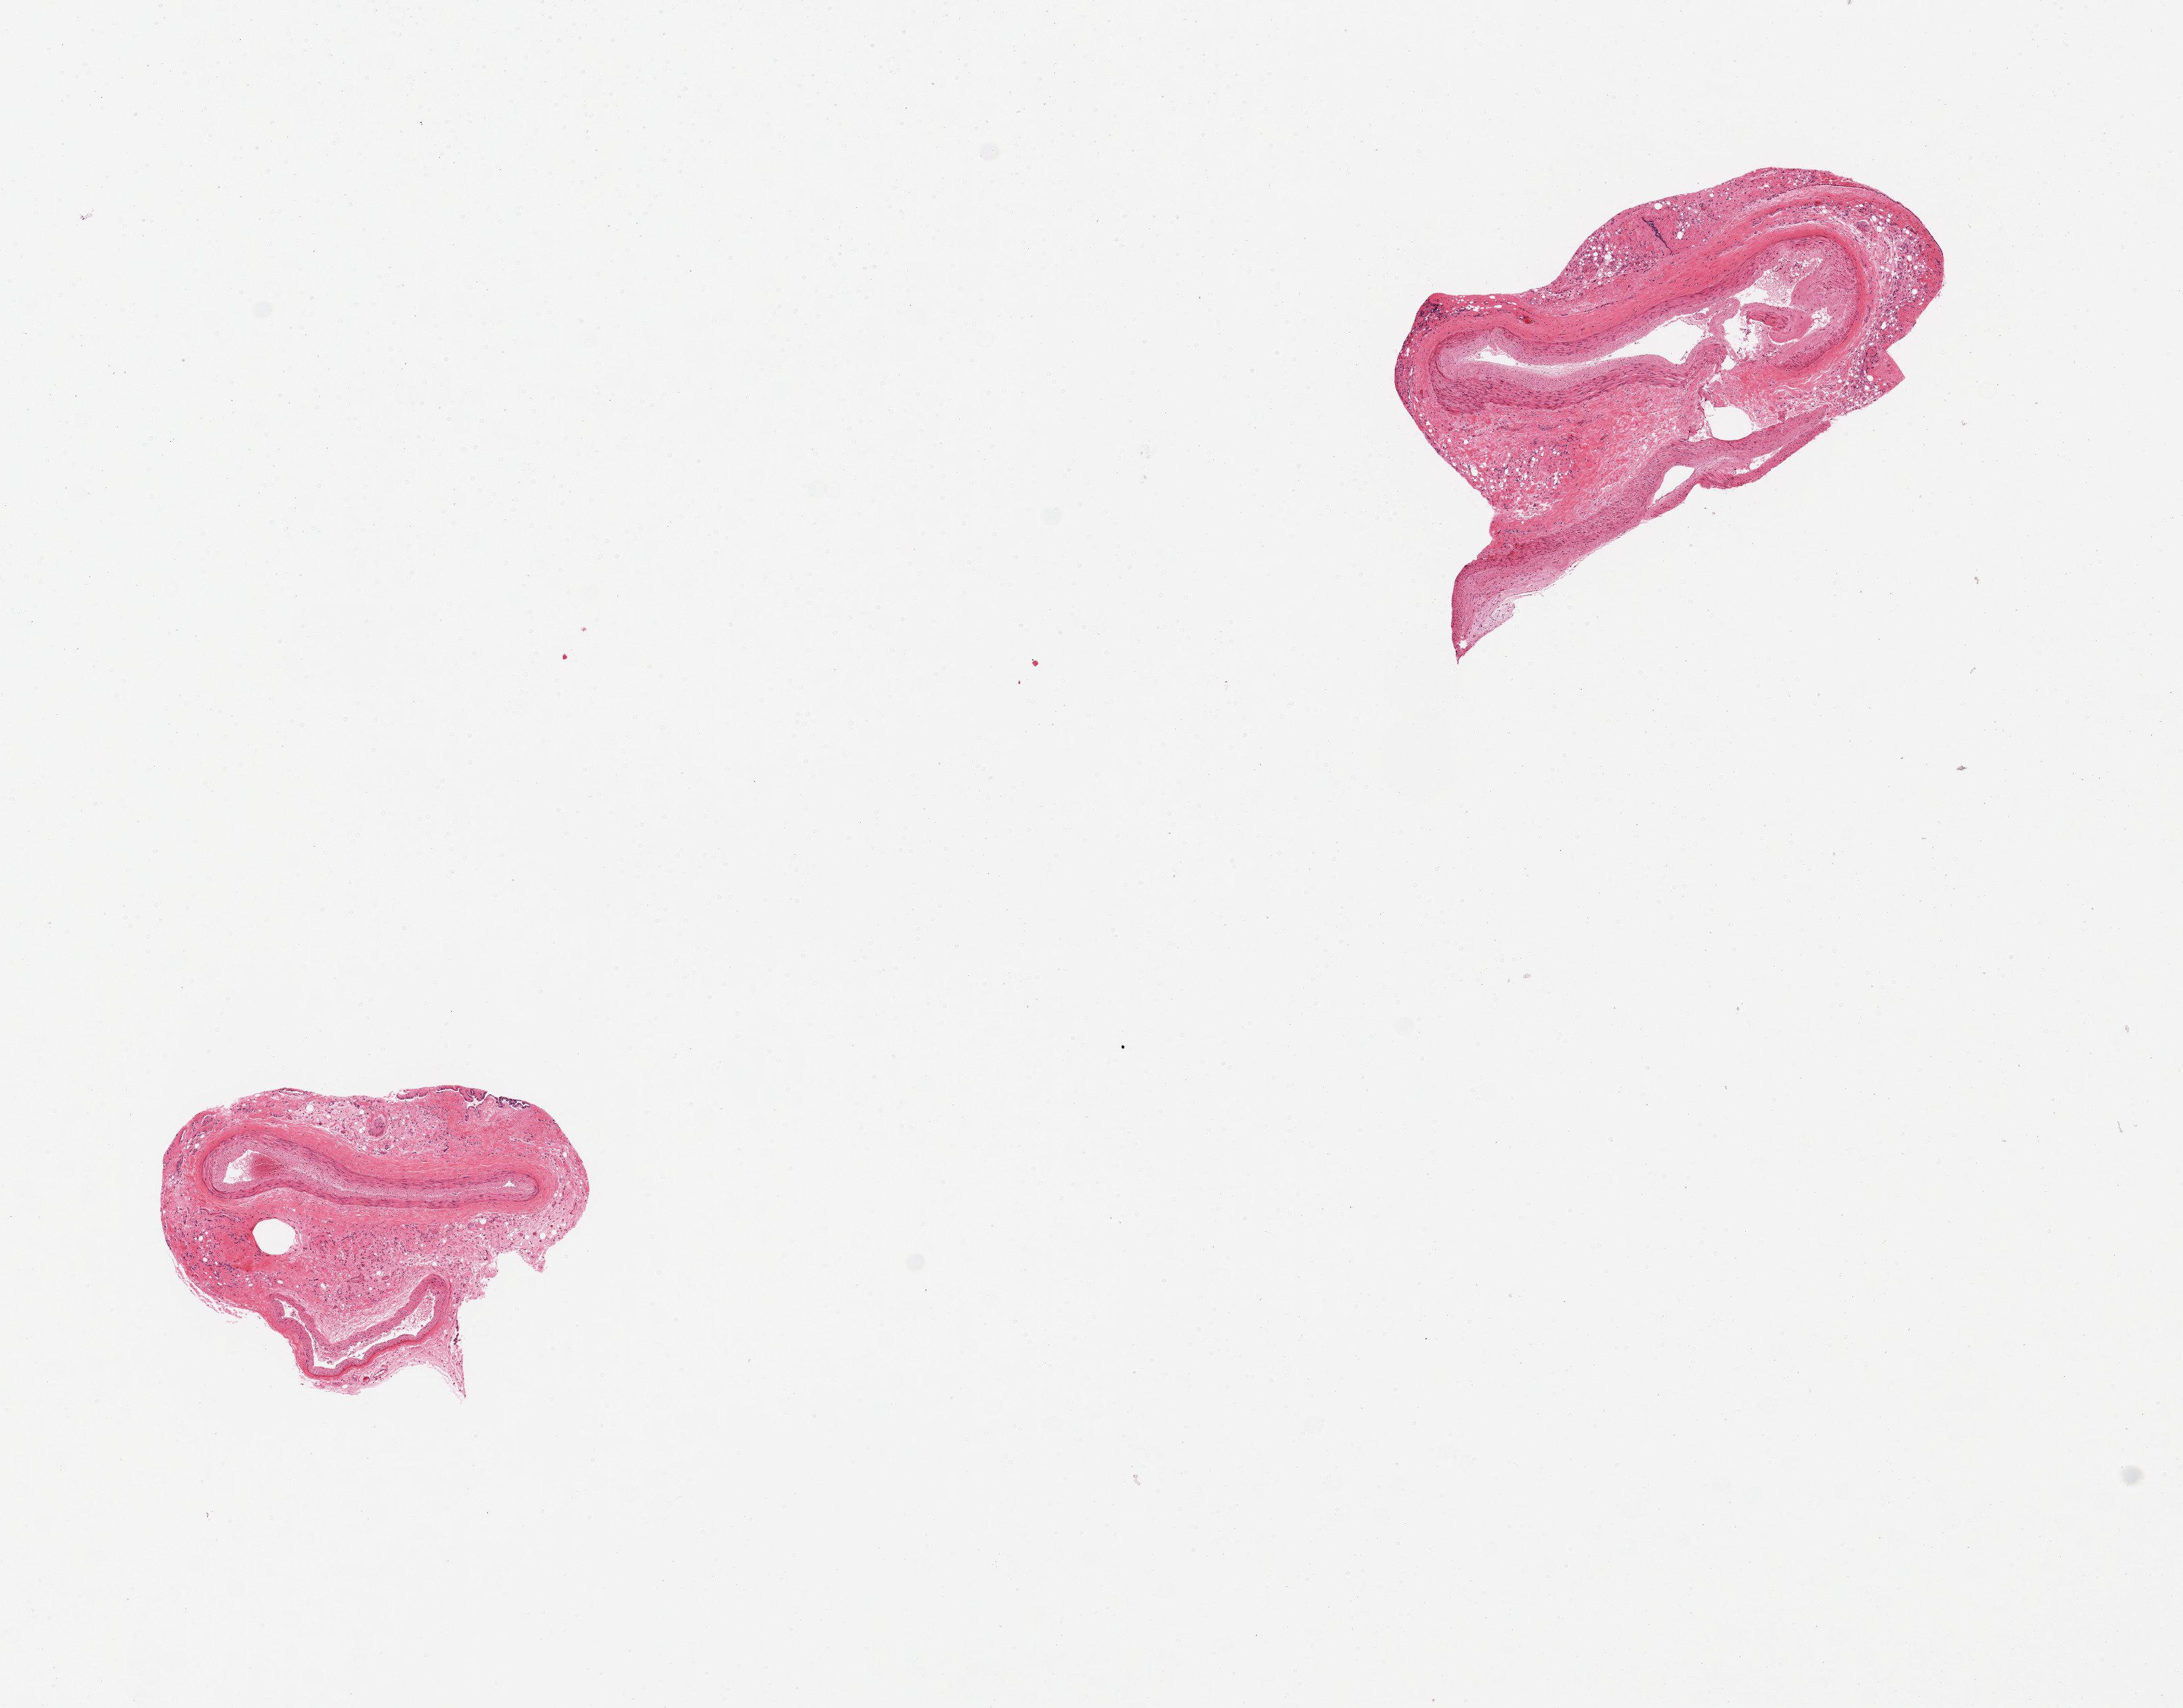
Digitized hematoxylin and eosin (H&E)-stained section — whole scanned area (about 12.8 x 10.0 mm, from a 20x scan) shown as a low-resolution overview, PAXgene-fixed paraffin-embedded (PFPE) section, sampled site (target tissue): coronary artery, tissue donor sample.
Review note (as recorded): 2 pieces, adherent connective tissue up to~1.5mm, circumerferential; minimal atherosis visible.